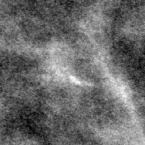
Region of interest cut from a scanned film mammogram (one marked finding); left breast; MLO view; BI-RADS breast density category 2 (scale 1–4).
Marked abnormality: calcifications, morphology fine linear branching, distribution clustered / linear; BI-RADS assessment category 4; pathology result (as recorded, not read from the image): malignant.